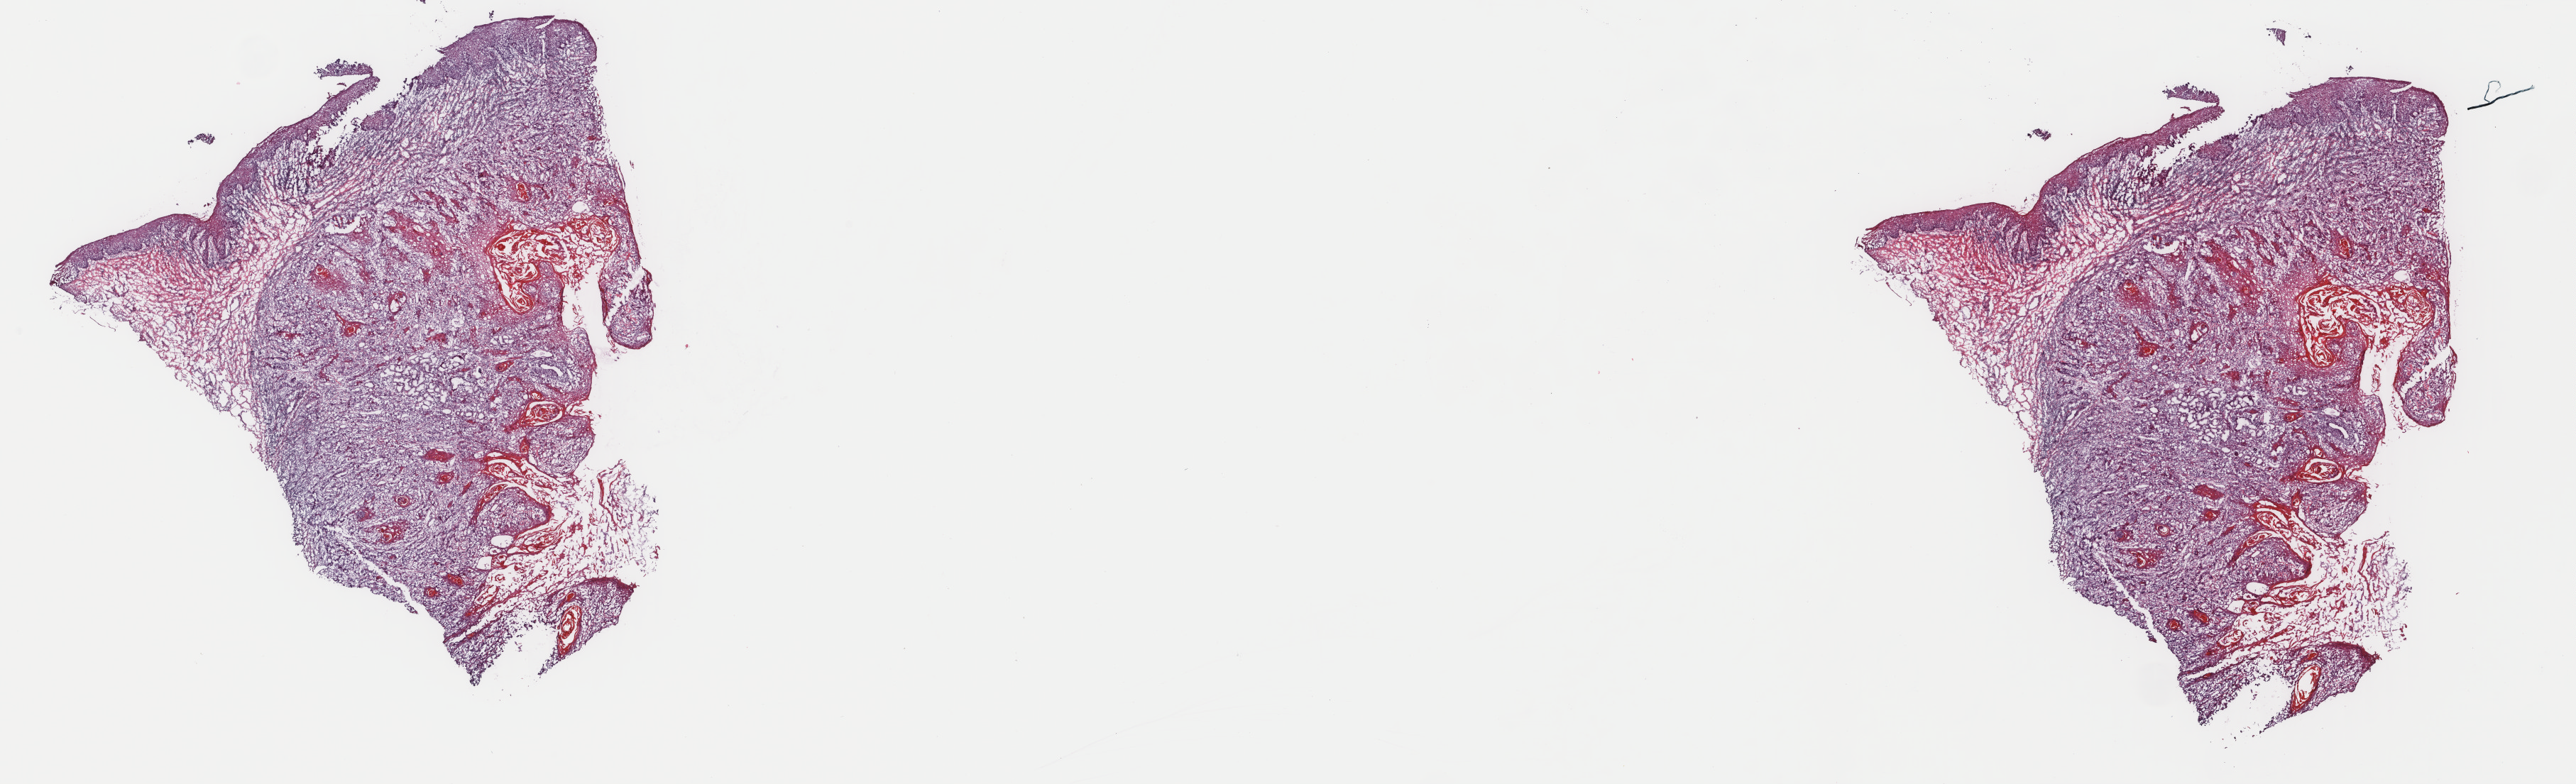
Digitized H&E tissue section (whole slide), a low-resolution overview of the entire scanned area, about 28.8 x 8.8 mm (acquisition: 40x scan); frozen section from the top of the tissue portion; head and neck, primary tumour sample. Patient: male, age at initial diagnosis 62 years. Histologic grade: G1 (well differentiated). Composition of this section per pathologist review: tumour cells 70%, tumour nuclei 70%, normal cells 25%, stromal cells 5%, necrosis 0%. Infiltration values recorded for this section: lymphocyte infiltration 10%, monocyte infiltration 0%, neutrophil infiltration 0%.
AJCC pathologic stage: III. Laterality: midline. Pathologic diagnosis: Squamous cell carcinoma, keratinizing, NOS (tongue, NOS).